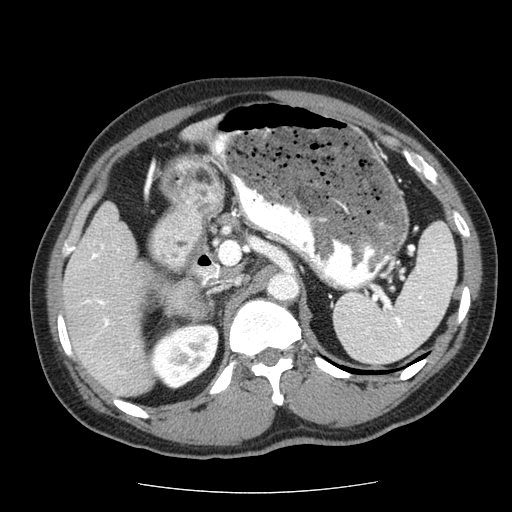
Contrast-enhanced abdominal CT (liver protocol), one axial slice. Slice 27 of 85 in the series (ordered by position). 120 kVp. Soft-tissue window (W 400 / L 40 HU). 512 × 512 image matrix. Case-level facts recorded for this patient, not image findings: diagnosis: hepatocellular carcinoma (patient treated with transarterial chemoembolisation; whether this scan precedes or follows treatment is not stated here); TNM stage (as recorded): Stage-IIIA; Child-Pugh class: A.
Outlined on this slice (semi-automatic segmentation, software-assisted and operator-edited):
- liver parenchyma outside the tumour (the mass and vessels are separate outlines, so this box may not span the whole liver): bounding box <62,202,154,396> (left, top, right, bottom; pixels)
- mass: <163,281,204,314>
- liver vessels: <82,244,120,328>